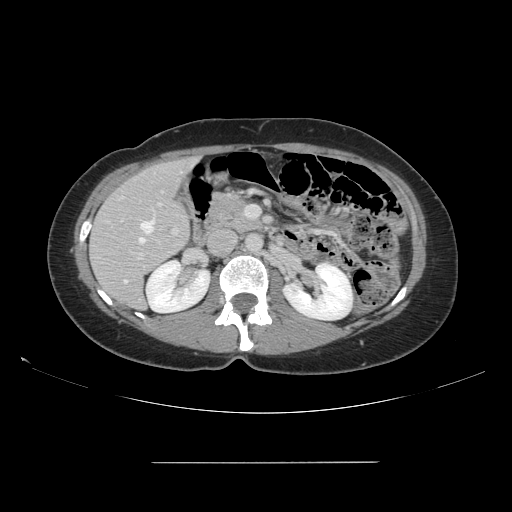
Contrast-enhanced abdominal CT, one axial slice; position 76 of 151 along the scan axis; intravenous contrast given; soft-tissue window (W 400 / L 40 HU); 2.5 mm slice thickness; 512 × 512 image matrix, field of view 421 × 421 mm. Female patient, age 46 years. Case-level facts recorded for this patient, not image findings: diagnosis: colorectal cancer liver metastases, imaged before liver resection; multiple liver metastases: yes; largest metastasis: 3 cm; chemotherapy before resection: no.
Annotated regions visible in this slice (outlined manually by an expert reader):
- hepatic veins: box from (x=125, y=220) to (x=155, y=282) px
- liver: (x=91, y=159)–(x=195, y=309)
- planned liver remnant (the part of the liver to remain after resection): (x=93, y=159)–(x=195, y=310)
- portal vein (with intrahepatic branches): (x=136, y=190)–(x=246, y=260)